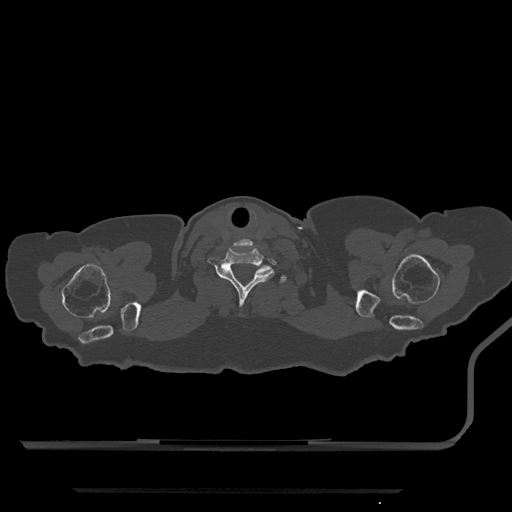
CT including the spine, one axial slice. Slice 736 of 797 in the series (ordered by position). Reconstruction kernel Br40s/3. Bone window (W 1800 / L 400 HU). 0.5 mm slice thickness. 512 × 512 image matrix, field of view 440 × 440 mm. Patient: female, 51 years. Case-level facts recorded for this patient, not image findings: primary cancer: neuro; vertebrae with lytic lesions (as recorded): T8.
Outlined on this slice (semi-automatic segmentation, software-assisted and operator-edited):
- T1 vertebra: box from (x=279, y=275) to (x=287, y=283) px